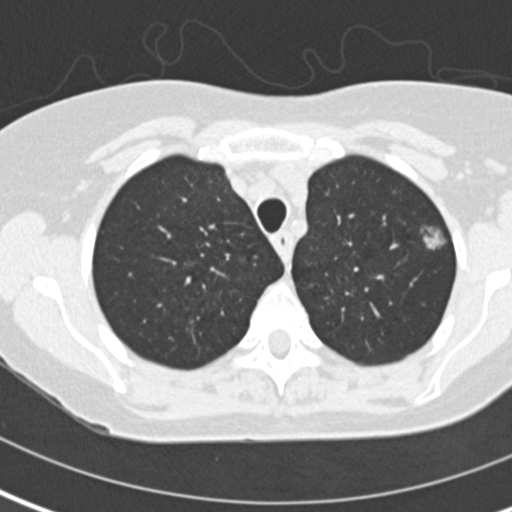
Low-dose screening chest CT, one axial slice. Slice 114 of 141 in the series (ordered by position). Reconstruction kernel B30f. Lung window (W 1500 / L -600 HU). 2 mm slice thickness. 512 × 512 image matrix, field of view 280 × 280 mm.
Annotated regions visible in this slice (expert manual segmentation):
- lesion 1 (tumor, upper lobe of left lung): bounding box <421,227,445,250> (left, top, right, bottom; pixels)